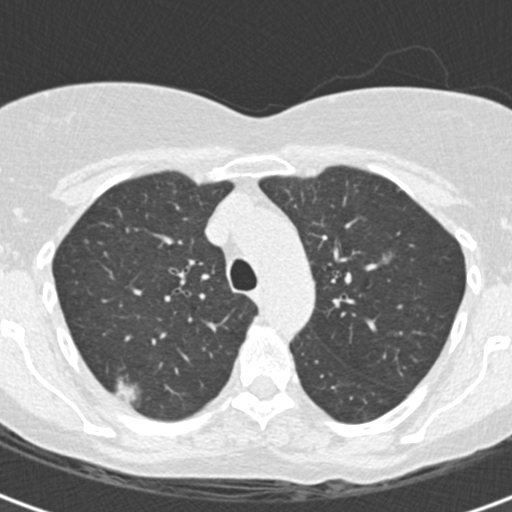
Low-dose screening chest CT, one axial slice; position 128 of 172 along the scan axis; 120 kVp; lung window (W 1500 / L -600 HU); 2 mm slice thickness; 512 × 512 image matrix, field of view 283 × 283 mm.
Structures marked on this image (manually delineated by an expert):
- lesion 1 (tumor, upper lobe of right lung): bounding box [x1, y1, x2, y2] px = [115, 376, 142, 407]